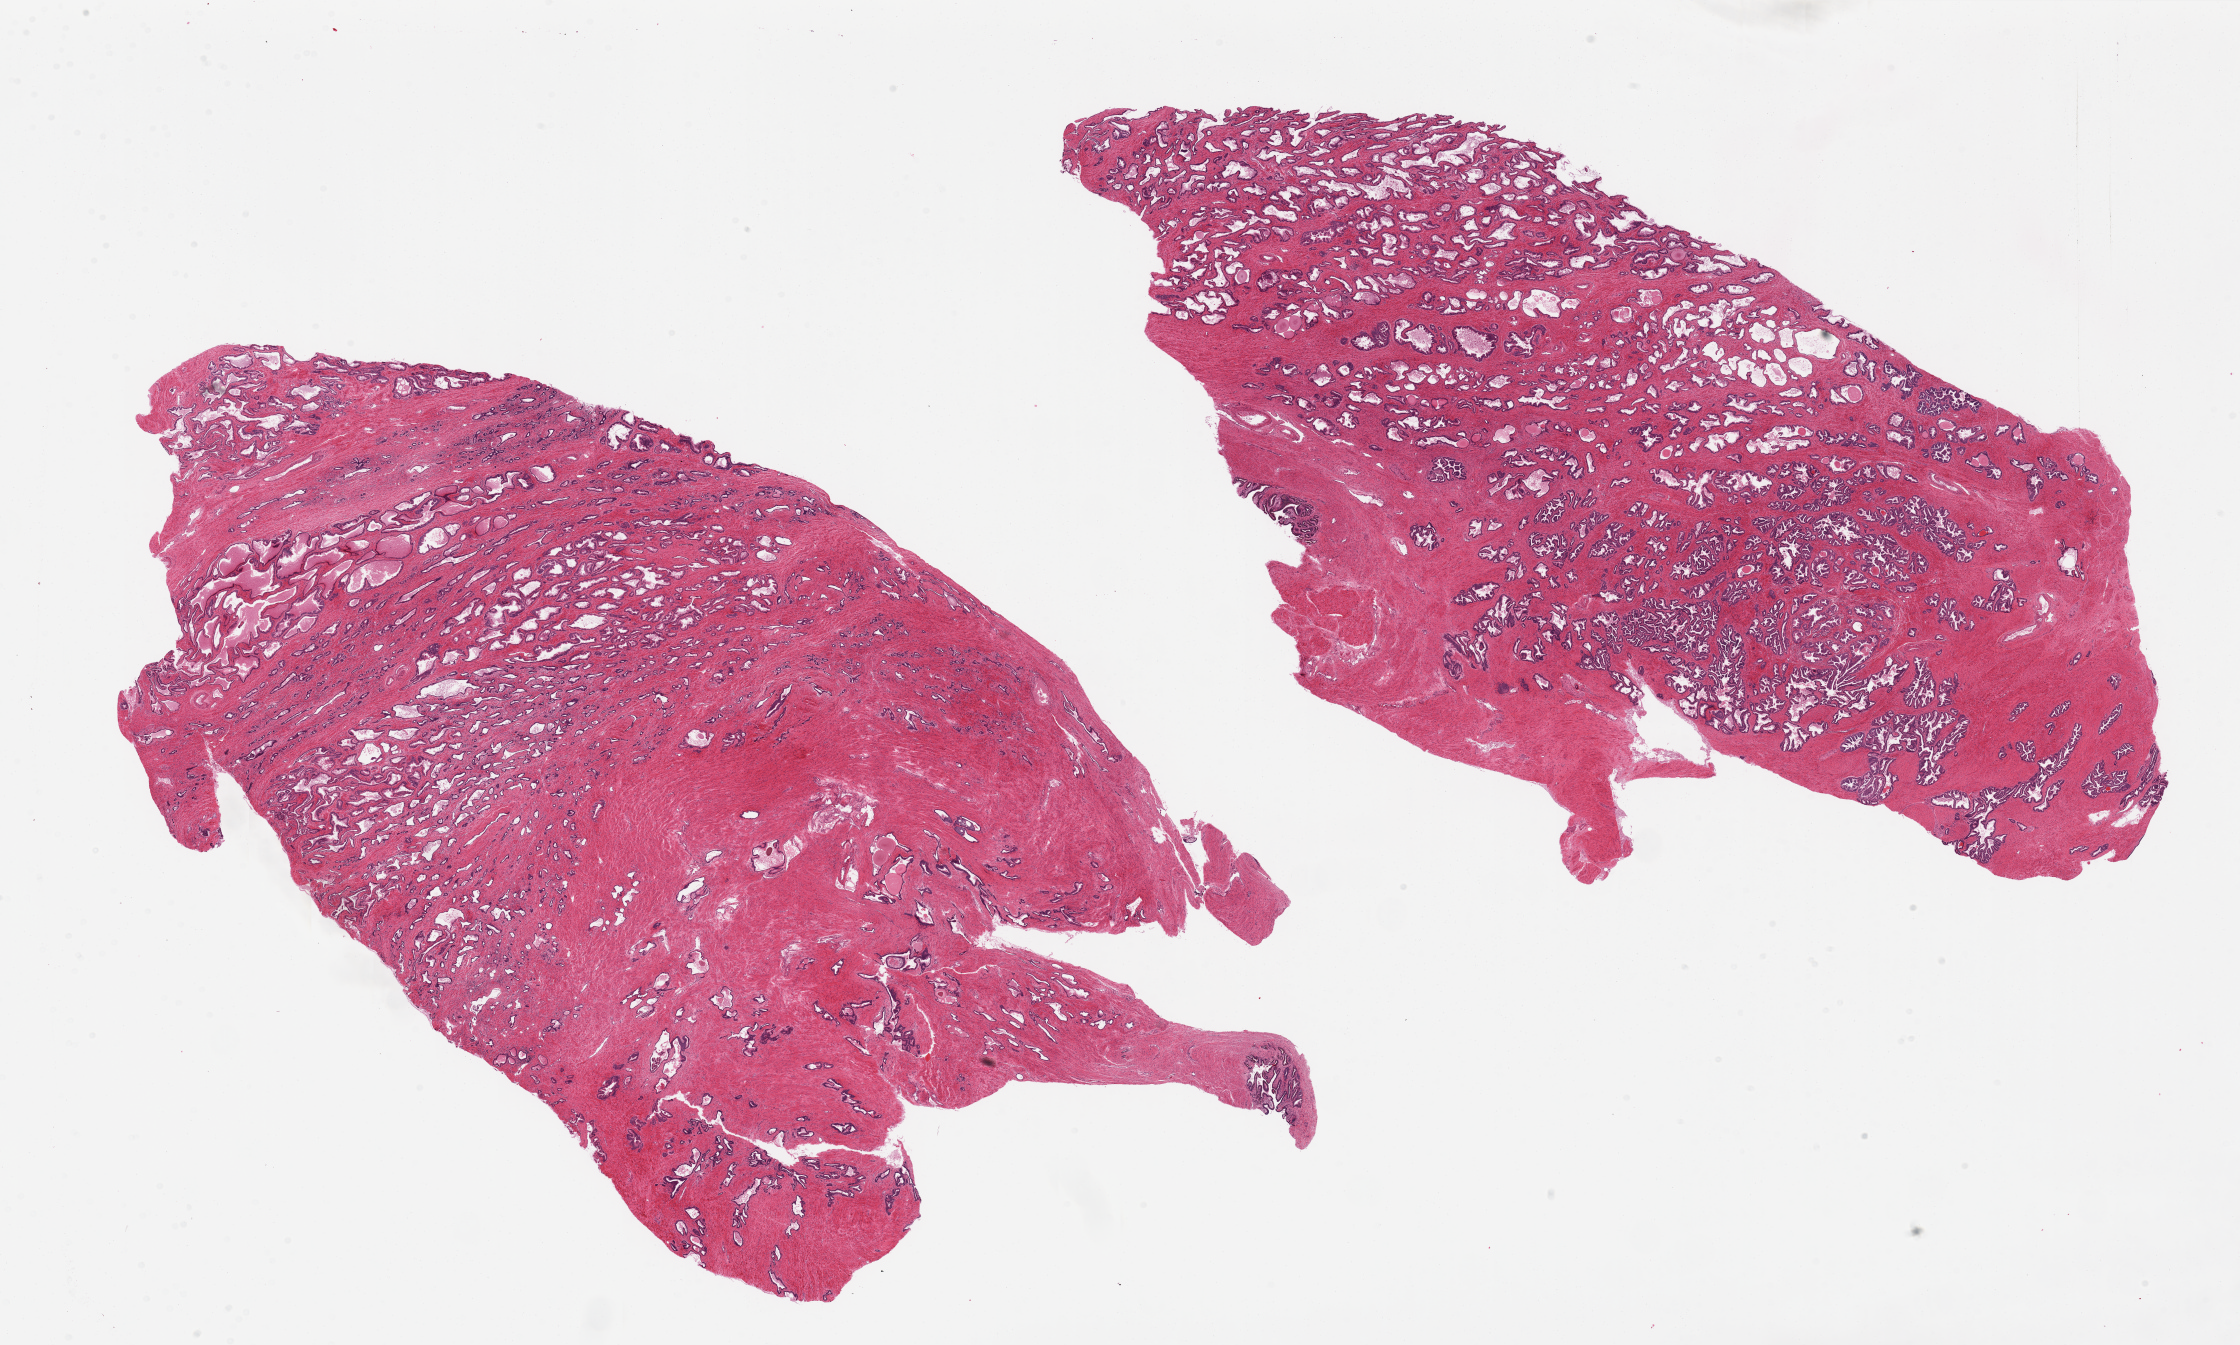
Whole-slide image, haematoxylin and eosin stain — shown as a low-resolution overview of the whole scanned area (about 35.4 x 21.3 mm), PAXgene-fixed paraffin-embedded (PFPE) section, section of prostate (target tissue), tissue donor sample.
- reviewer comment on this tissue sample: 2 pieces, patchy chronic prostatitis, portion of seminal vesicle